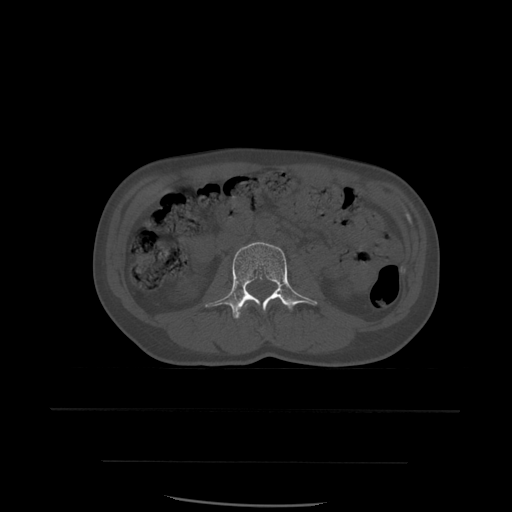
CT including the spine, one axial slice; position 202 of 574 along the scan axis; bone window (W 1800 / L 400 HU); 1.25 mm slice thickness; 512 × 512 image matrix, field of view 392 × 392 mm. Patient age 48 years. From the clinical record (not read from this slice): primary cancer: lung; vertebrae with lytic lesions (as recorded): T11.
Annotated regions visible in this slice (semi-automatically segmented with operator editing):
- L2 vertebra: bounding box <240,298,277,330> (left, top, right, bottom; pixels)
- L3 vertebra: <206,242,318,320>